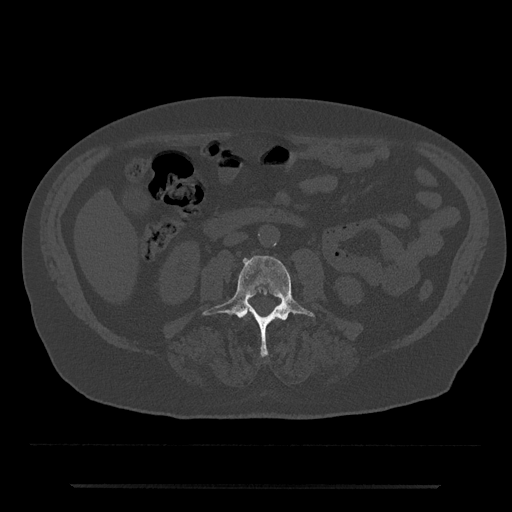
CT including the spine, one axial slice. Position 413 of 797 along the scan axis. Reconstruction kernel Br40s/3. Bone window (W 1800 / L 400 HU). 512 × 512 image matrix, field of view 434 × 434 mm. Patient: male, 80 years. Case-level facts recorded for this patient, not image findings: primary cancer: prostate.
Annotated regions visible in this slice (semi-automatically segmented with operator editing):
- L3 vertebra: bounding box [x1, y1, x2, y2] px = [202, 255, 315, 357]